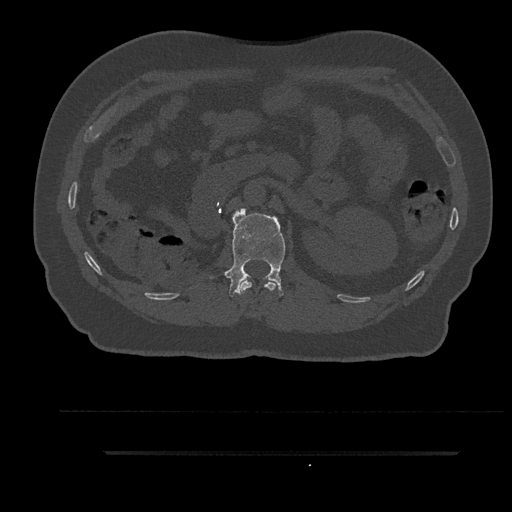
CT including the spine, one axial slice; slice 188 of 797 in the series (ordered by position); bone window (W 1800 / L 400 HU); 512 × 512 image matrix, field of view 432 × 432 mm. Male patient, age 63 years. Case-level facts recorded for this patient, not image findings: primary cancer: renal.
Structures marked on this image (semi-automatic segmentation, software-assisted and operator-edited):
- L1 vertebra: box from (x=225, y=208) to (x=286, y=297) px
- T12 vertebra: (x=240, y=280)–(x=278, y=294)